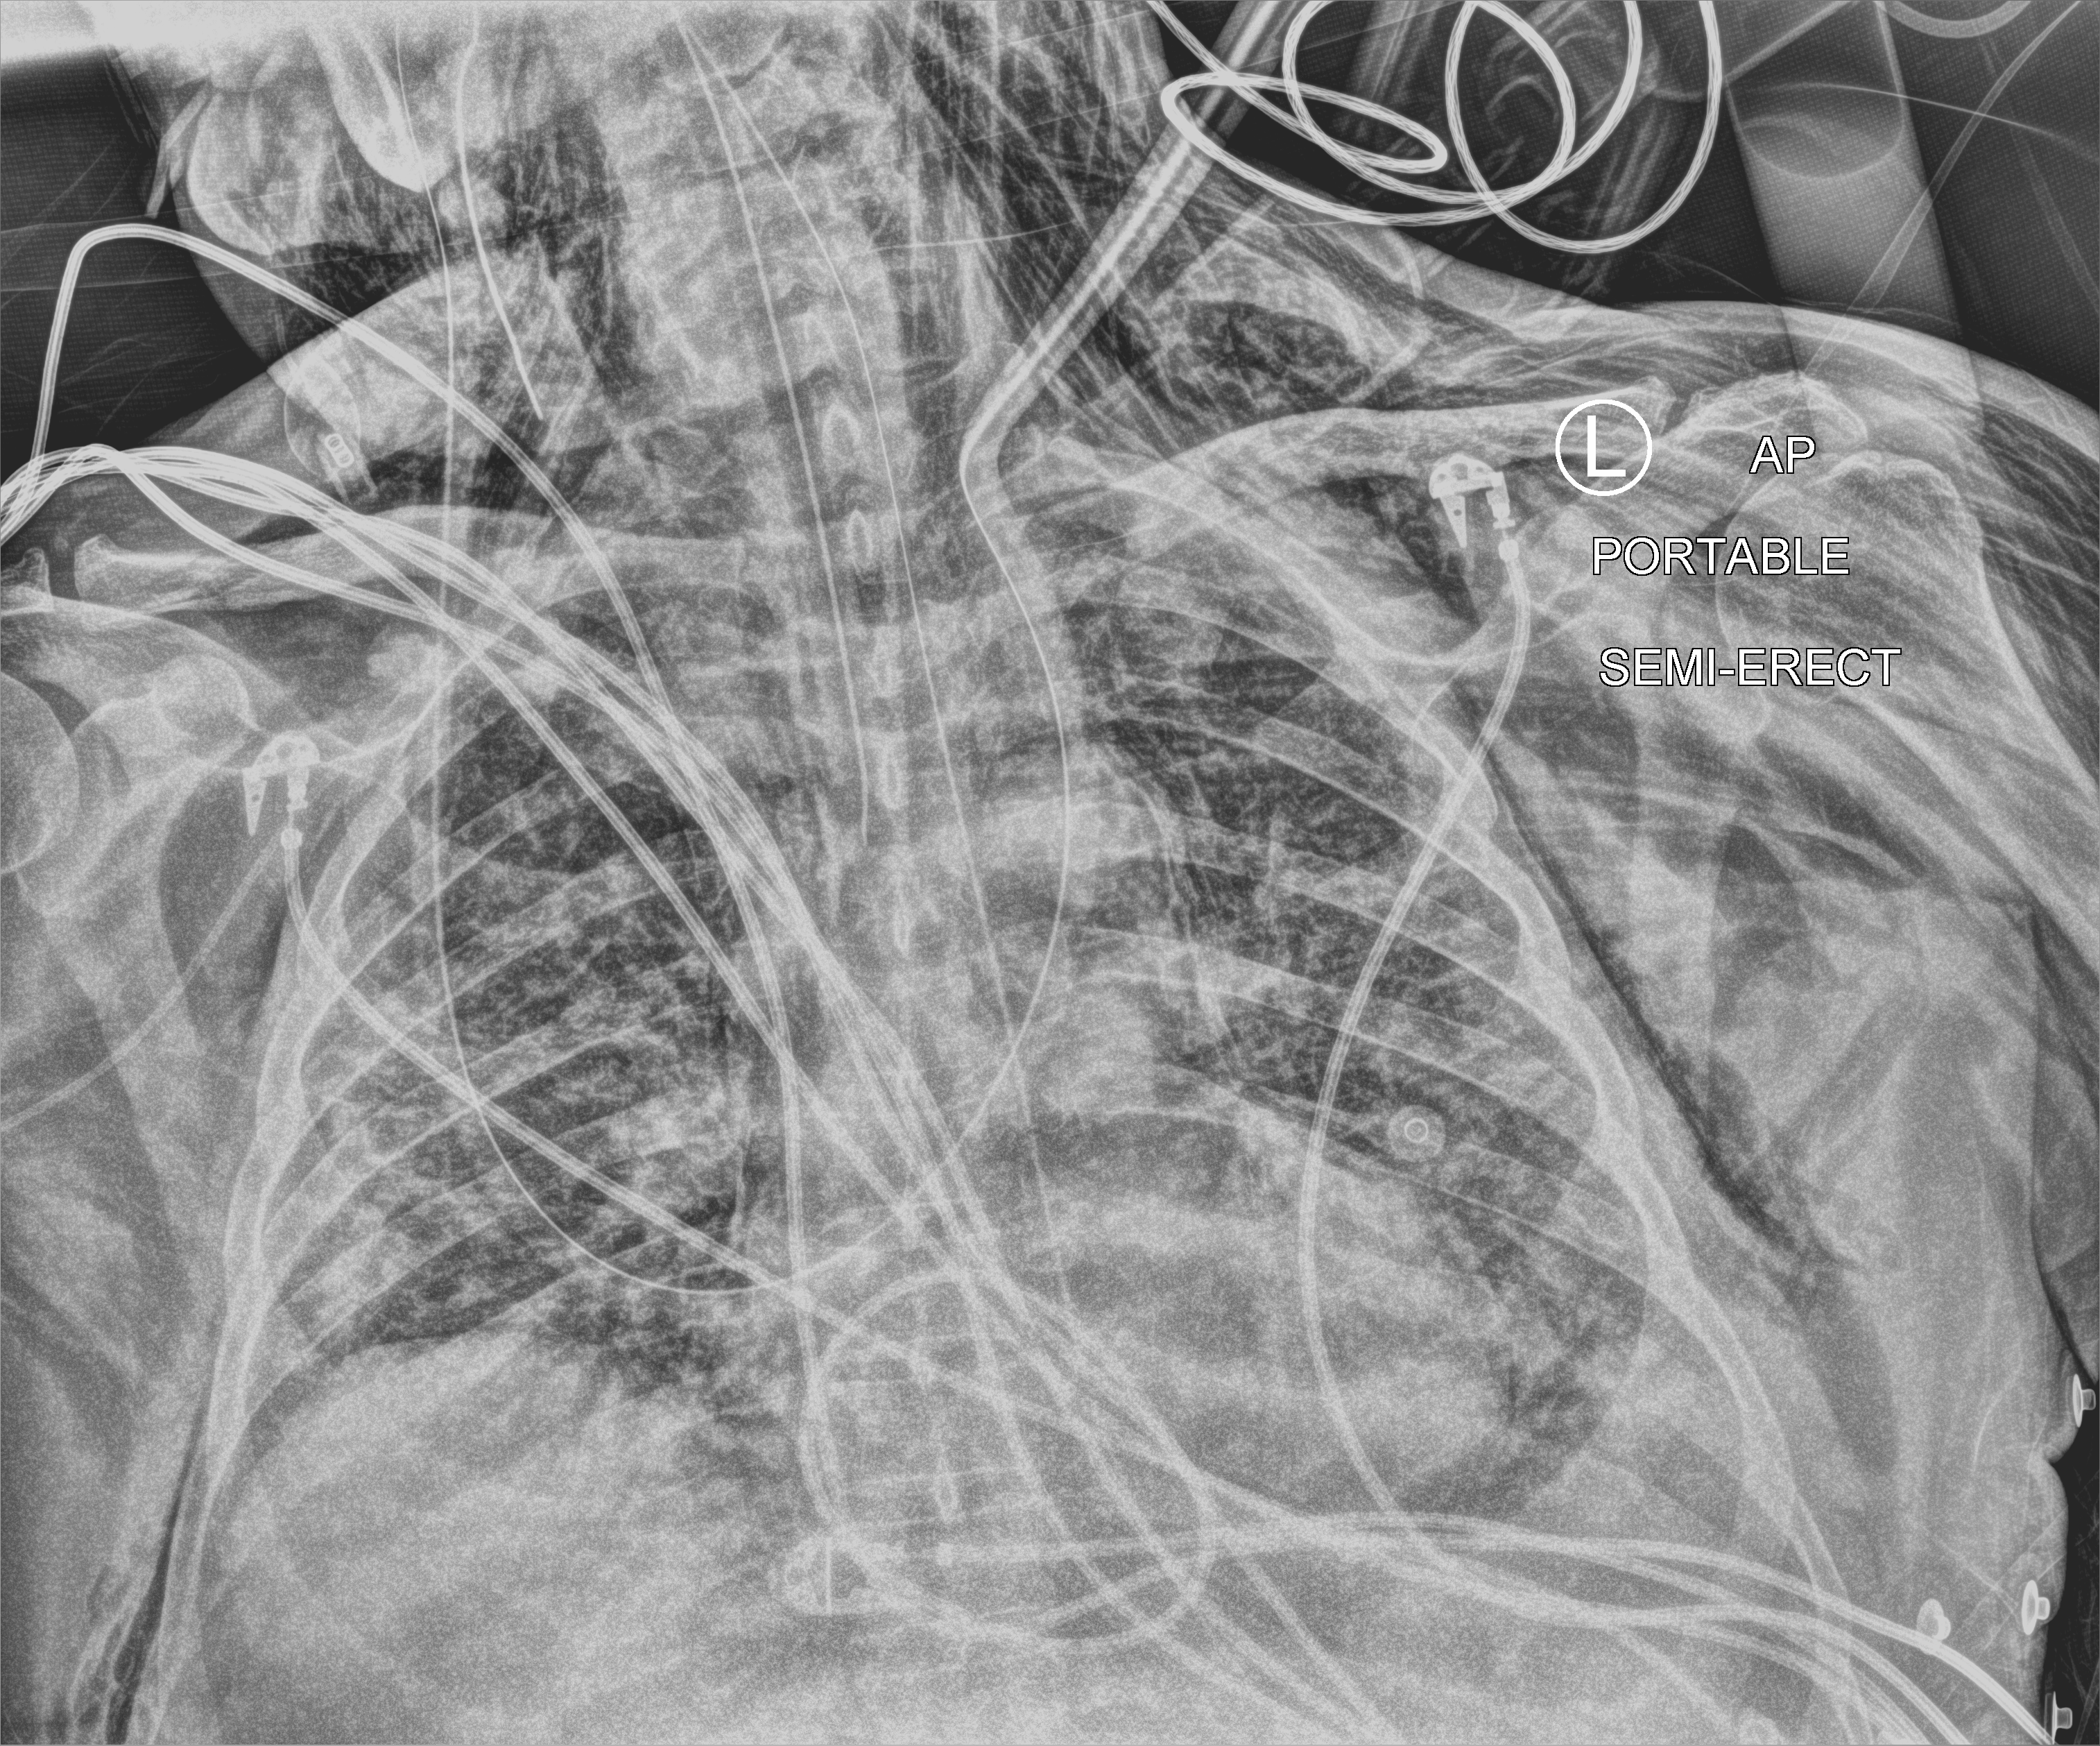
Portable chest radiograph, anteroposterior (AP) projection. Male patient hospitalised with COVID-19, age 60–74 years.
From the hospital-stay record, not from the radiograph (when in the stay this image was taken is not recorded):
- mechanically ventilated during this hospital stay: yes